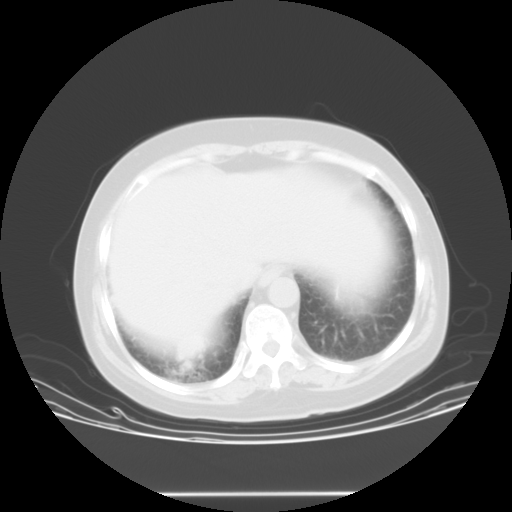
Chest CT, one axial slice. Position 3 of 23 along the scan axis. Reconstruction kernel STANDARD. Lung window (W 1500 / L -600 HU). 512 × 512 image matrix, field of view 408 × 408 mm. Female patient, age 55 years. Case-level facts recorded for this patient, not image findings: clinical TNM (as recorded): T2 N0 M1b.
Outlined on this slice (bounding box drawn by a radiologist):
- lung tumour (recorded histology: squamous cell carcinoma): box from (x=167, y=327) to (x=215, y=376) px